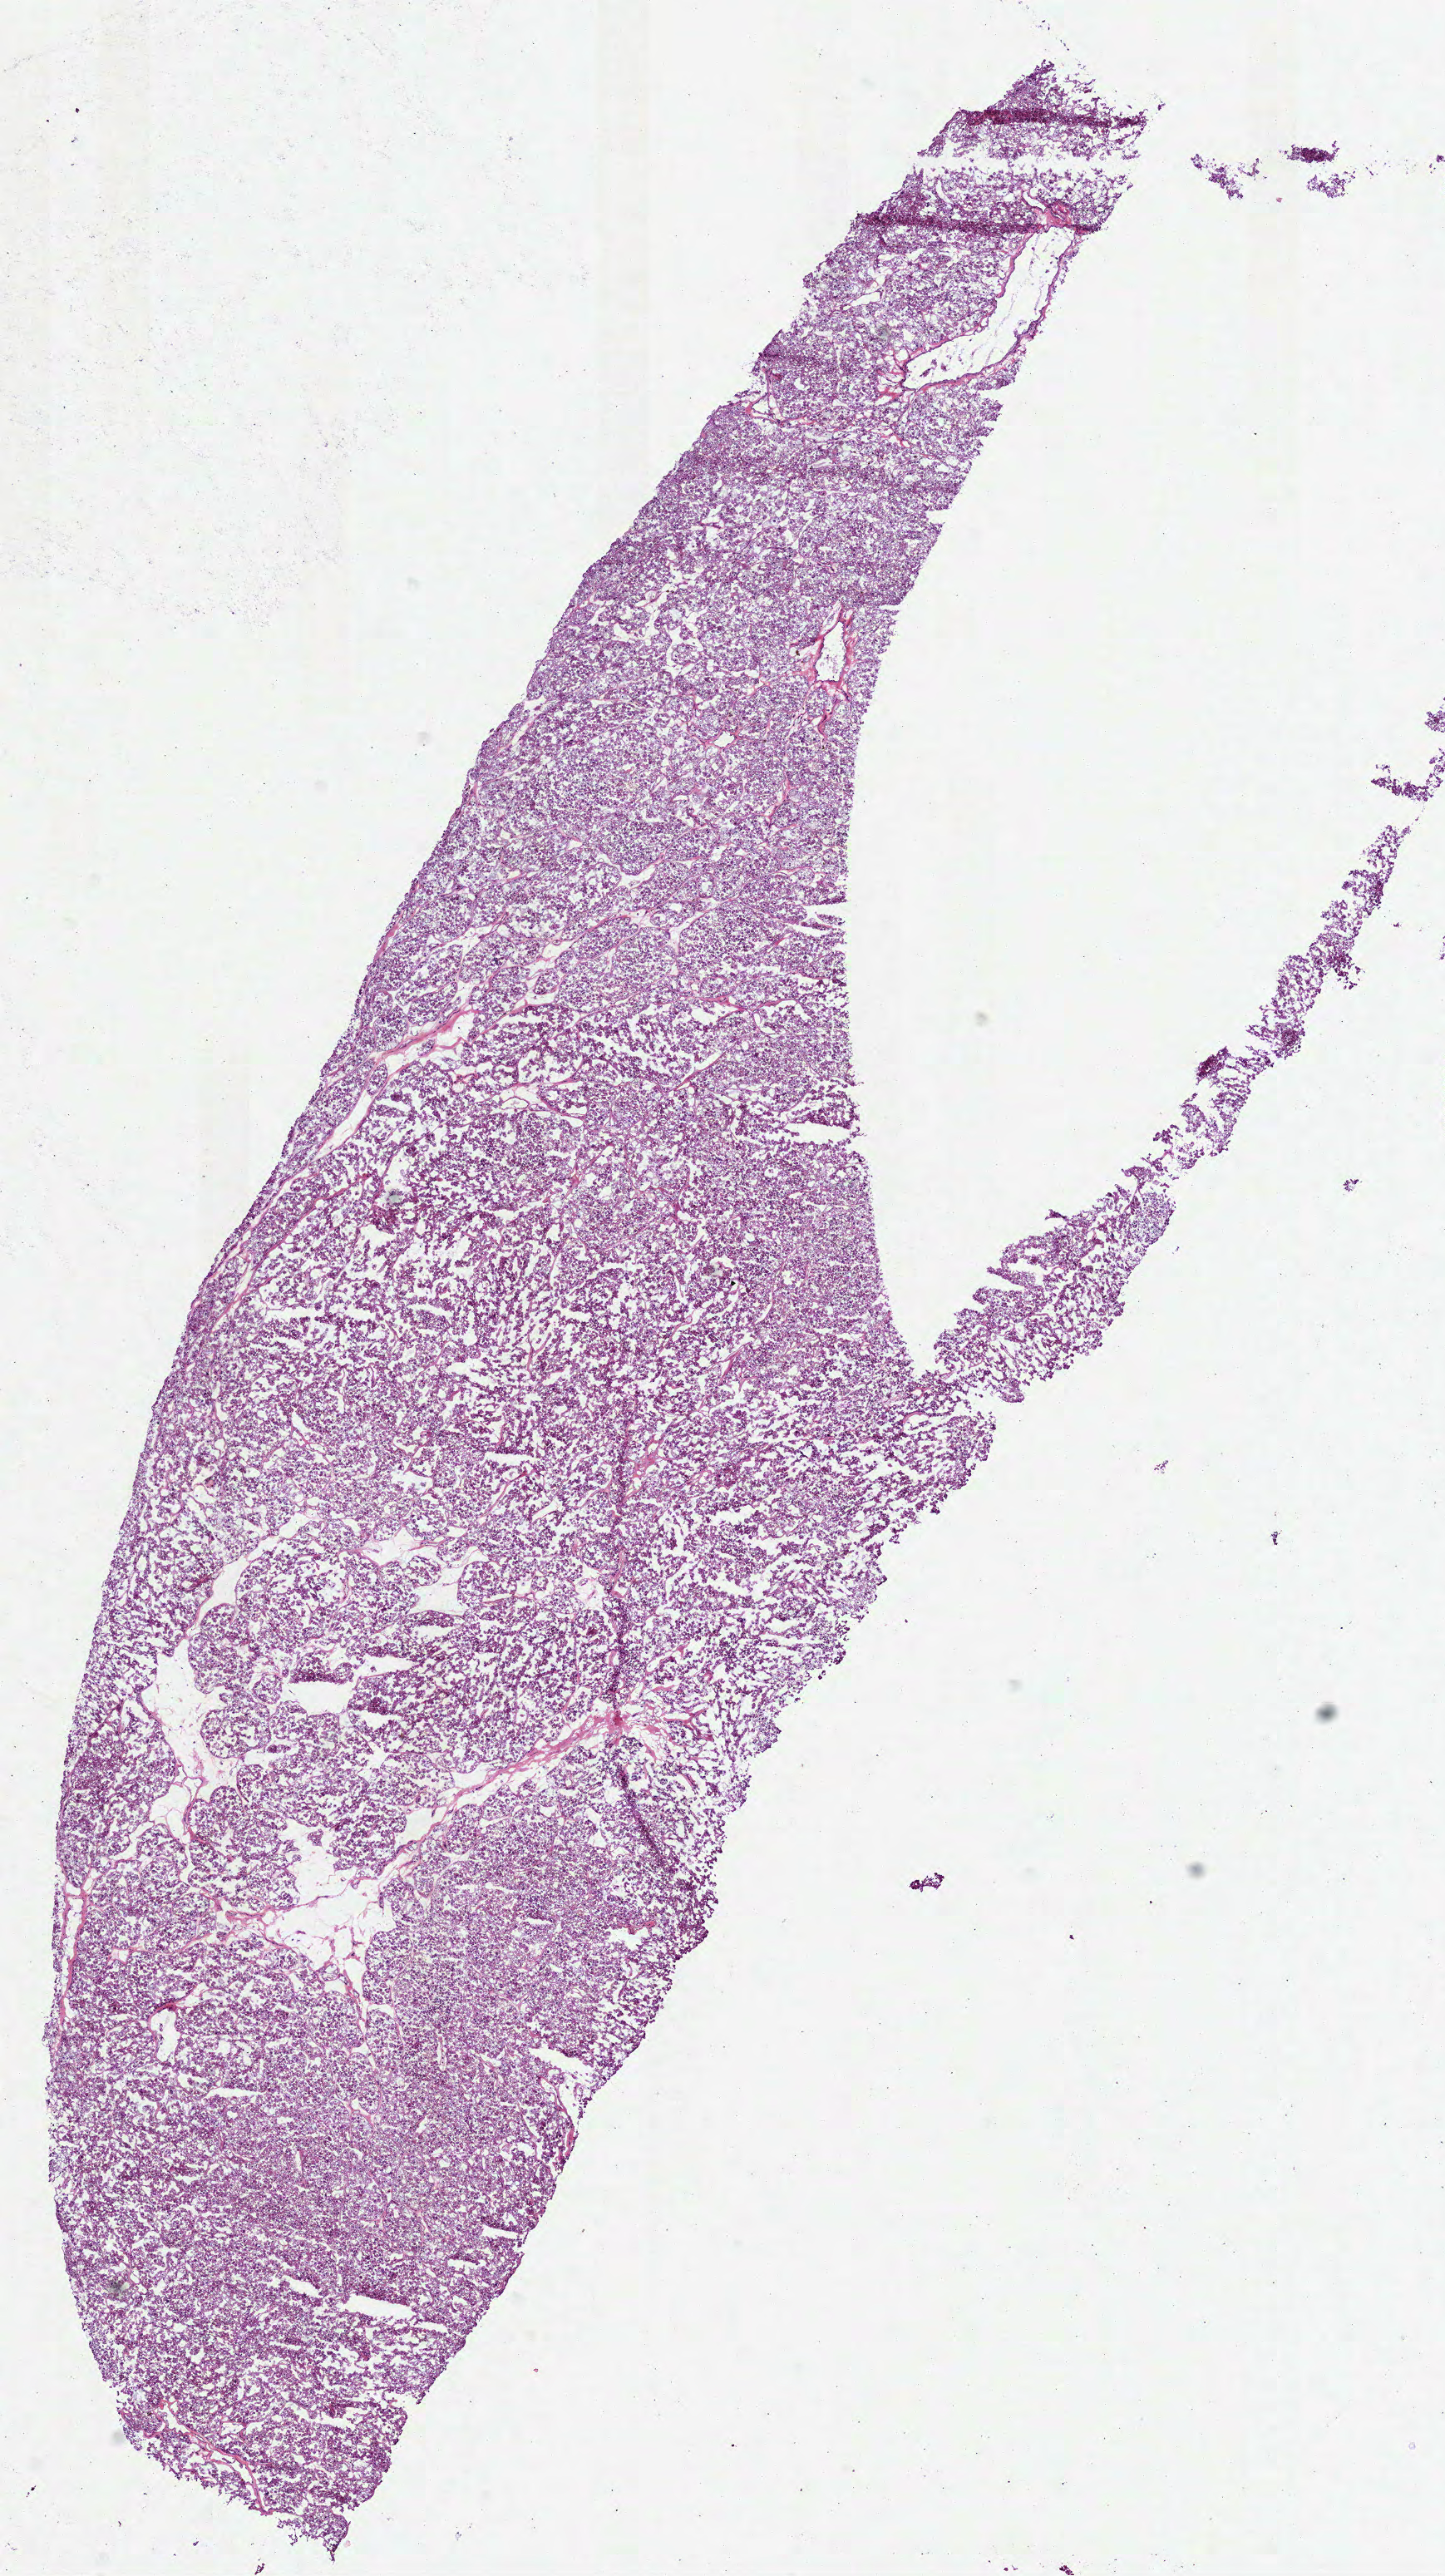
Digitized H&E tissue section (whole slide) — low-resolution overview of the scanned area, about 7.0 x 12.5 mm (slide scanned at 40x). Frozen section from the bottom of the tissue portion. Kidney, primary tumour sample. Female, age 41 years at initial diagnosis. Slide review estimates, as recorded: tumour cells 100%, tumour nuclei 95%, normal cells 0%, stromal cells 0%, necrosis 0%. Infiltration values recorded for this section: lymphocyte infiltration 0%, monocyte infiltration 0%, neutrophil infiltration 0%.
- AJCC pathologic stage: II
- TNM: T2 N0
- diagnosis: Renal cell carcinoma, chromophobe type
- lymph nodes positive (case pathology): 0 of 3 examined